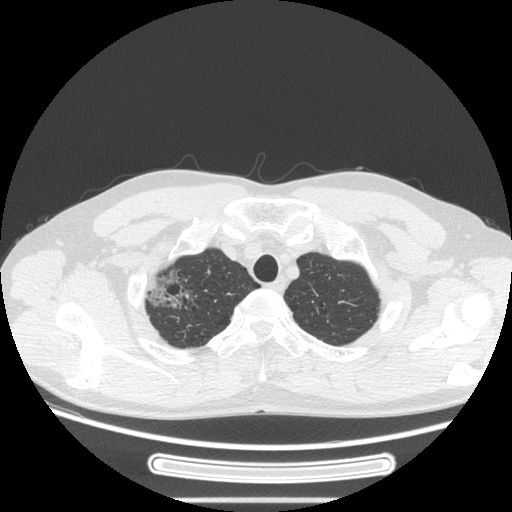
Chest CT, one axial slice. Position 231 of 269 along the scan axis. Reconstruction kernel STANDARD. 120 kVp. Lung window (W 1500 / L -600 HU). 512 × 512 image matrix. Patient: male, 53 years. From the clinical record (not read from this slice): clinical TNM (as recorded): T1c N0 M0.
Outlined on this slice (rectangle marked by the reading radiologist):
- lung tumour (recorded histology: adenocarcinoma): bounding box (x1, y1, x2, y2) in pixels: (131, 250, 208, 323)